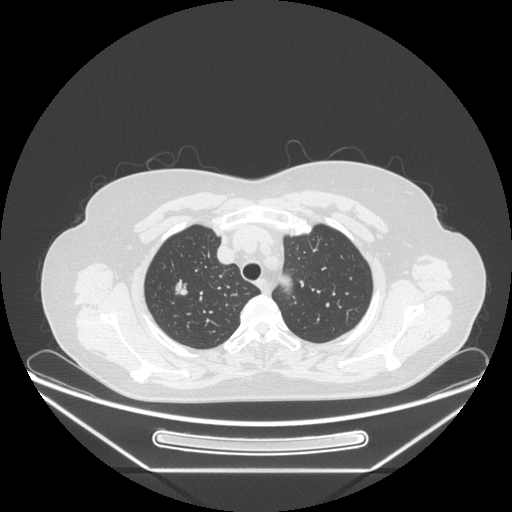
Chest CT, one axial slice; position 199 of 236 along the scan axis; reconstruction kernel STANDARD; lung window (W 1500 / L -600 HU); 512 × 512 image matrix. Female patient, age 60 years. From the clinical record (not read from this slice): clinical TNM (as recorded): T1c N0 M0.
Structures marked on this image (bounding box drawn by a radiologist):
- lung tumour (recorded histology: adenocarcinoma): bounding box [x1, y1, x2, y2] px = [169, 272, 198, 303]